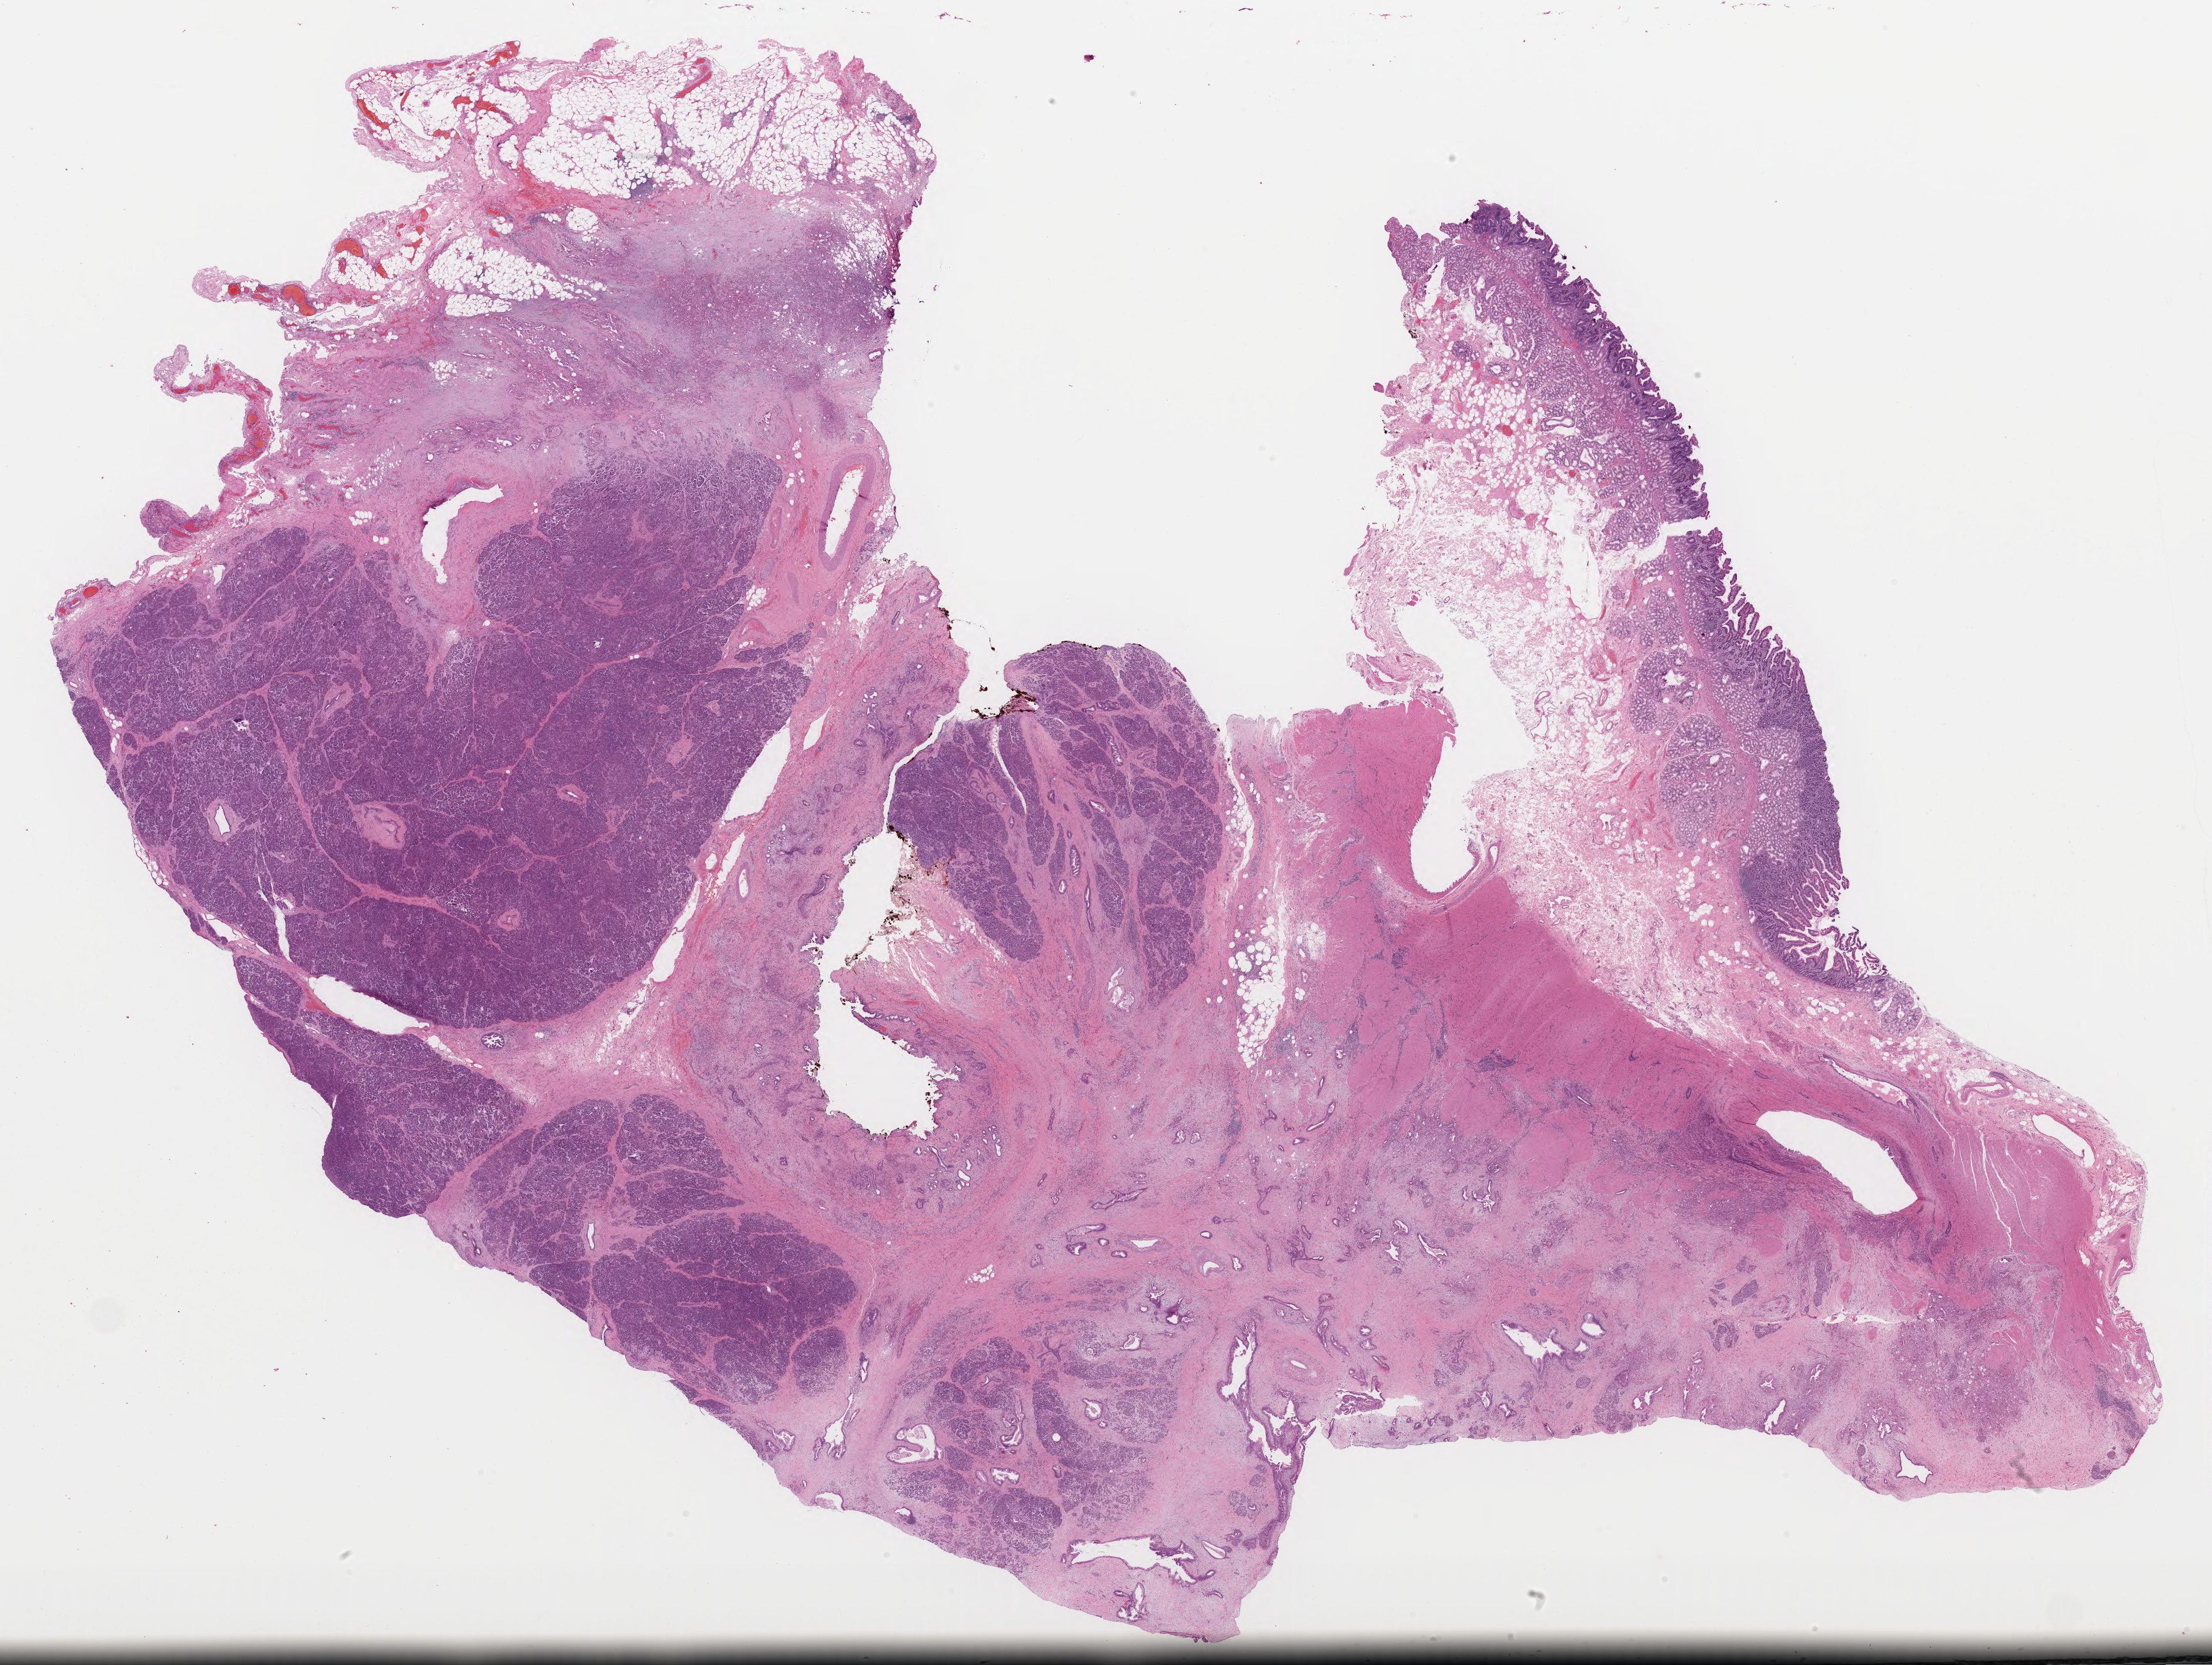
Digitized H&E-stained tissue section (whole slide) — a low-resolution overview of the entire scanned area, about 29.7 x 22.4 mm; formalin-fixed paraffin-embedded (FFPE) diagnostic section; sample: primary tumour, pancreas. Patient: female, age at initial diagnosis 54 years. Histologic grade: G1 (well differentiated).
AJCC pathologic stage: IIB (7th edition). Pathologic diagnosis: Infiltrating duct carcinoma, NOS. Lymph nodes positive (case pathology): 2 of 21 examined.